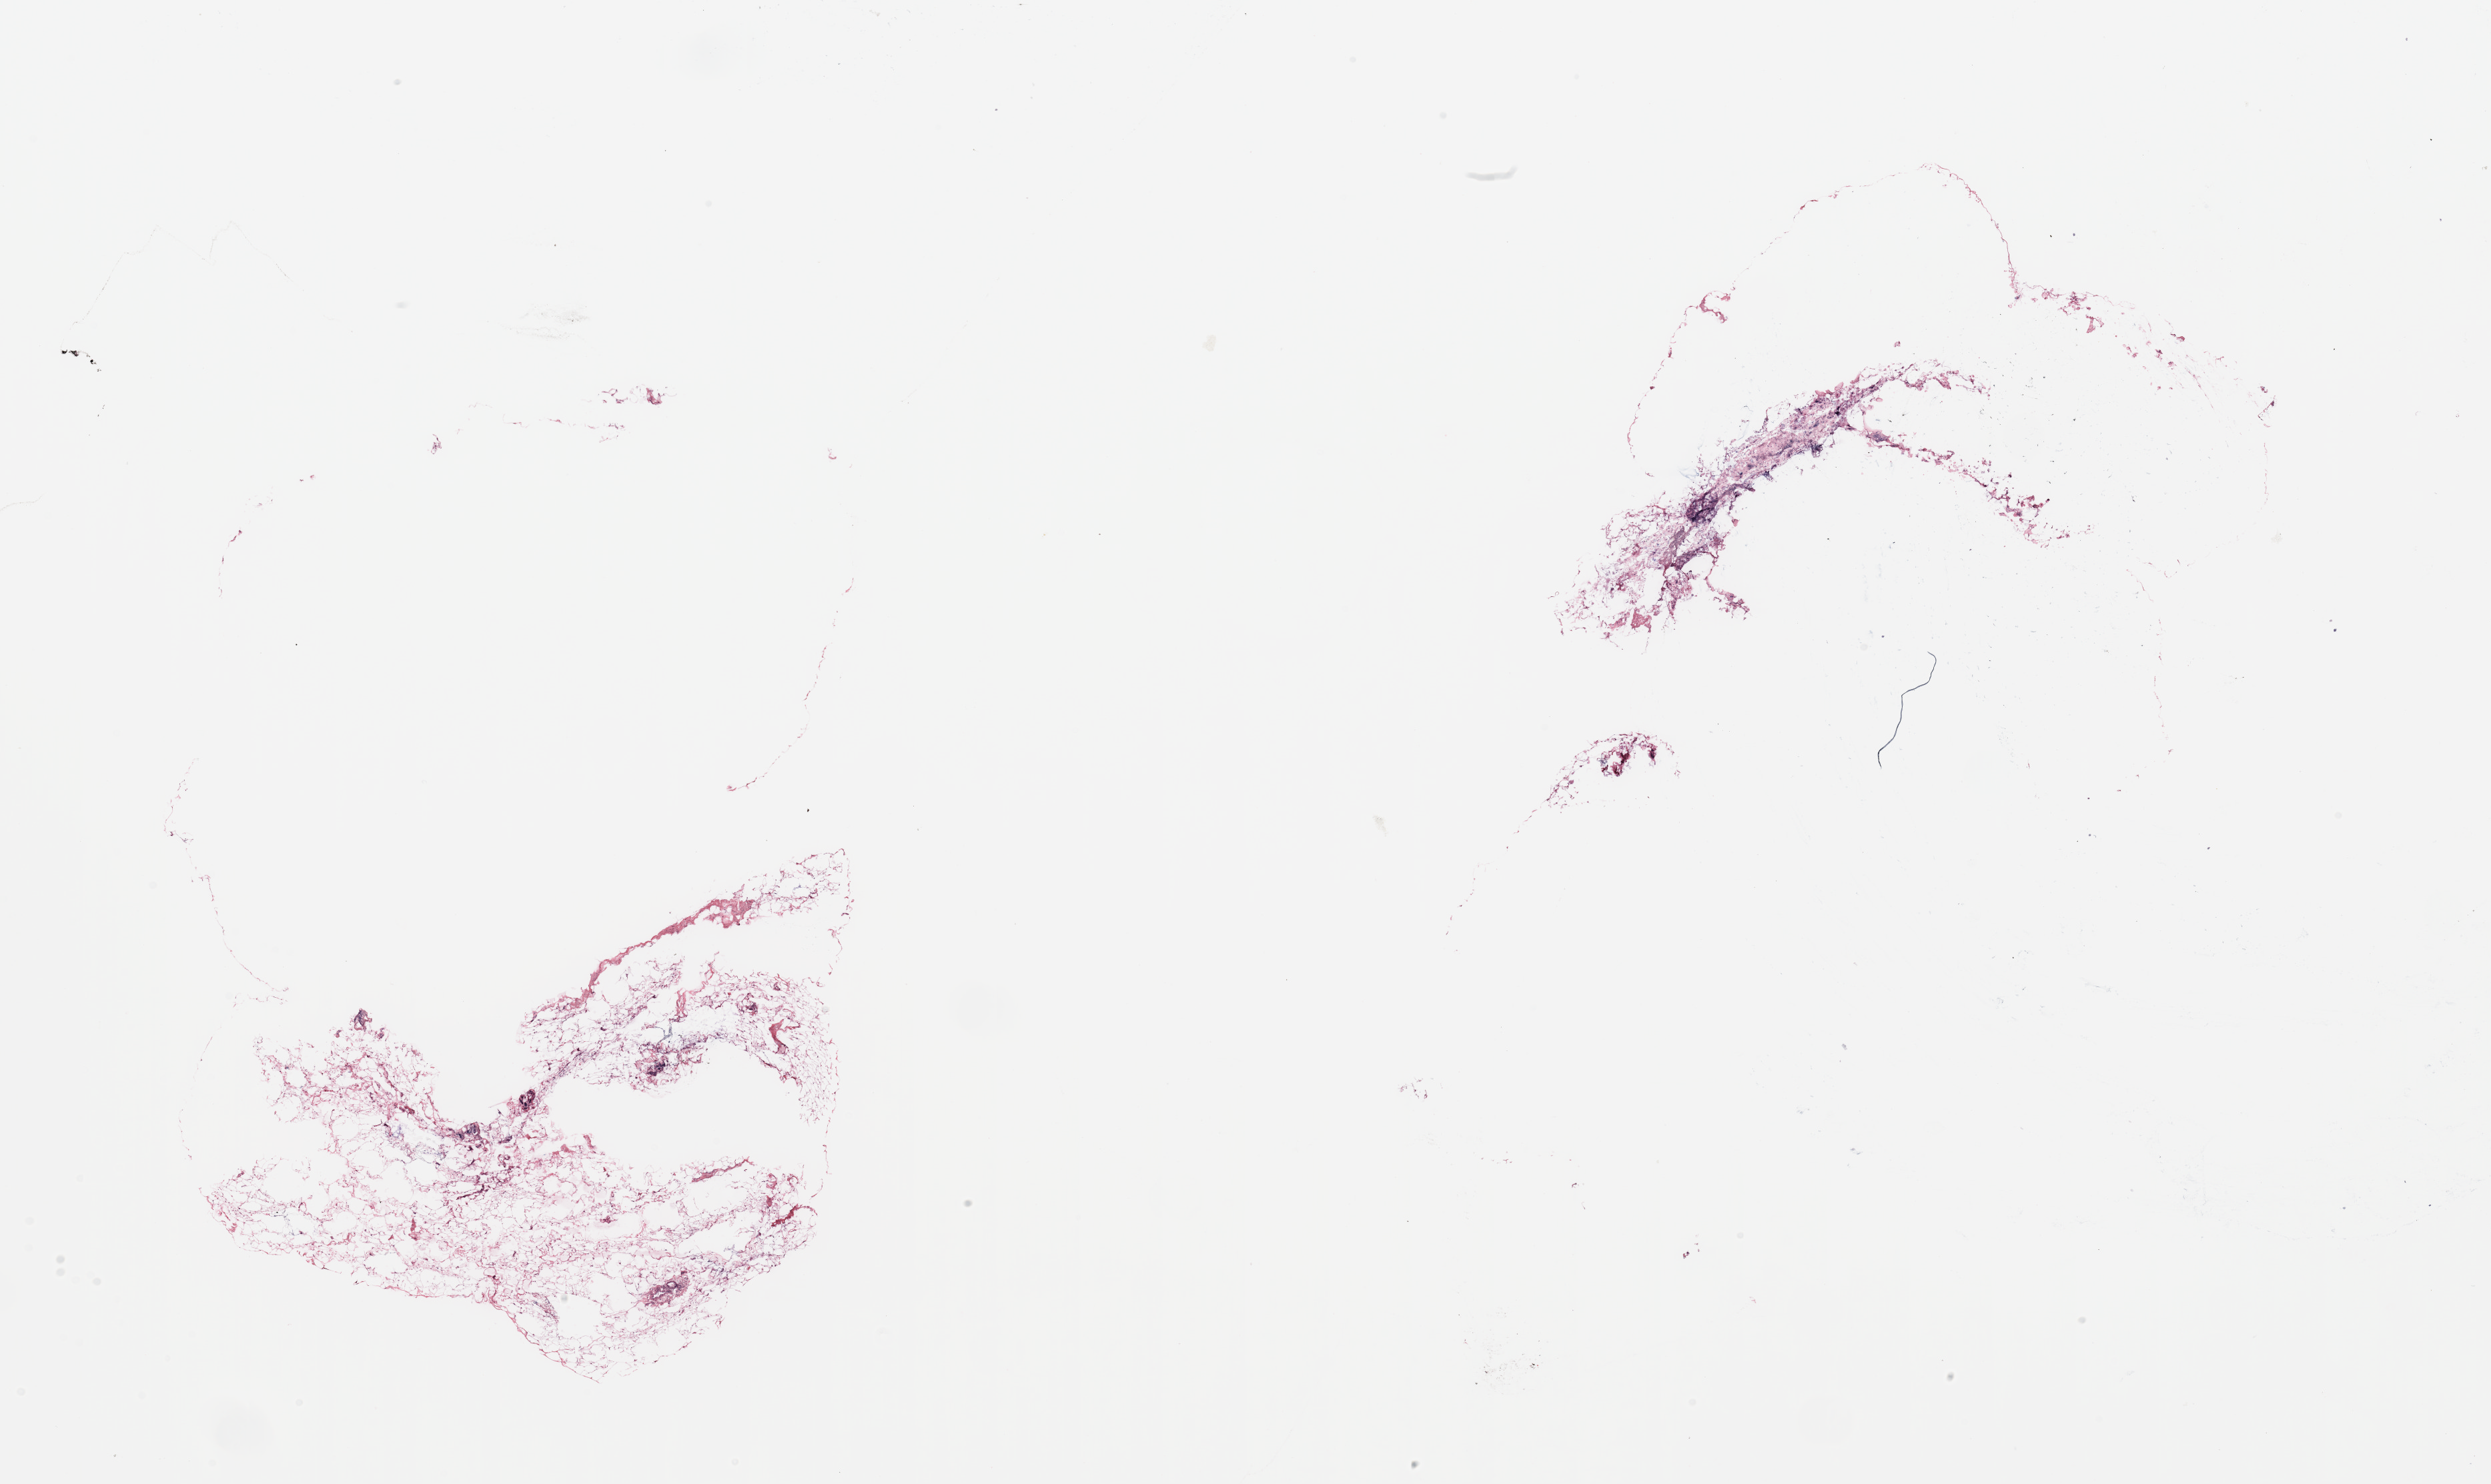
Digitized Hematoxylin and eosin (H&E) stained tissue section (whole slide) — low-resolution overview of the scanned area, about 29.5 x 17.6 mm, tumour tissue sample, breast. Female, 60 y/o.
AJCC pathologic stage: IIA. Histologic diagnosis: Infiltrating duct carcinoma, NOS.